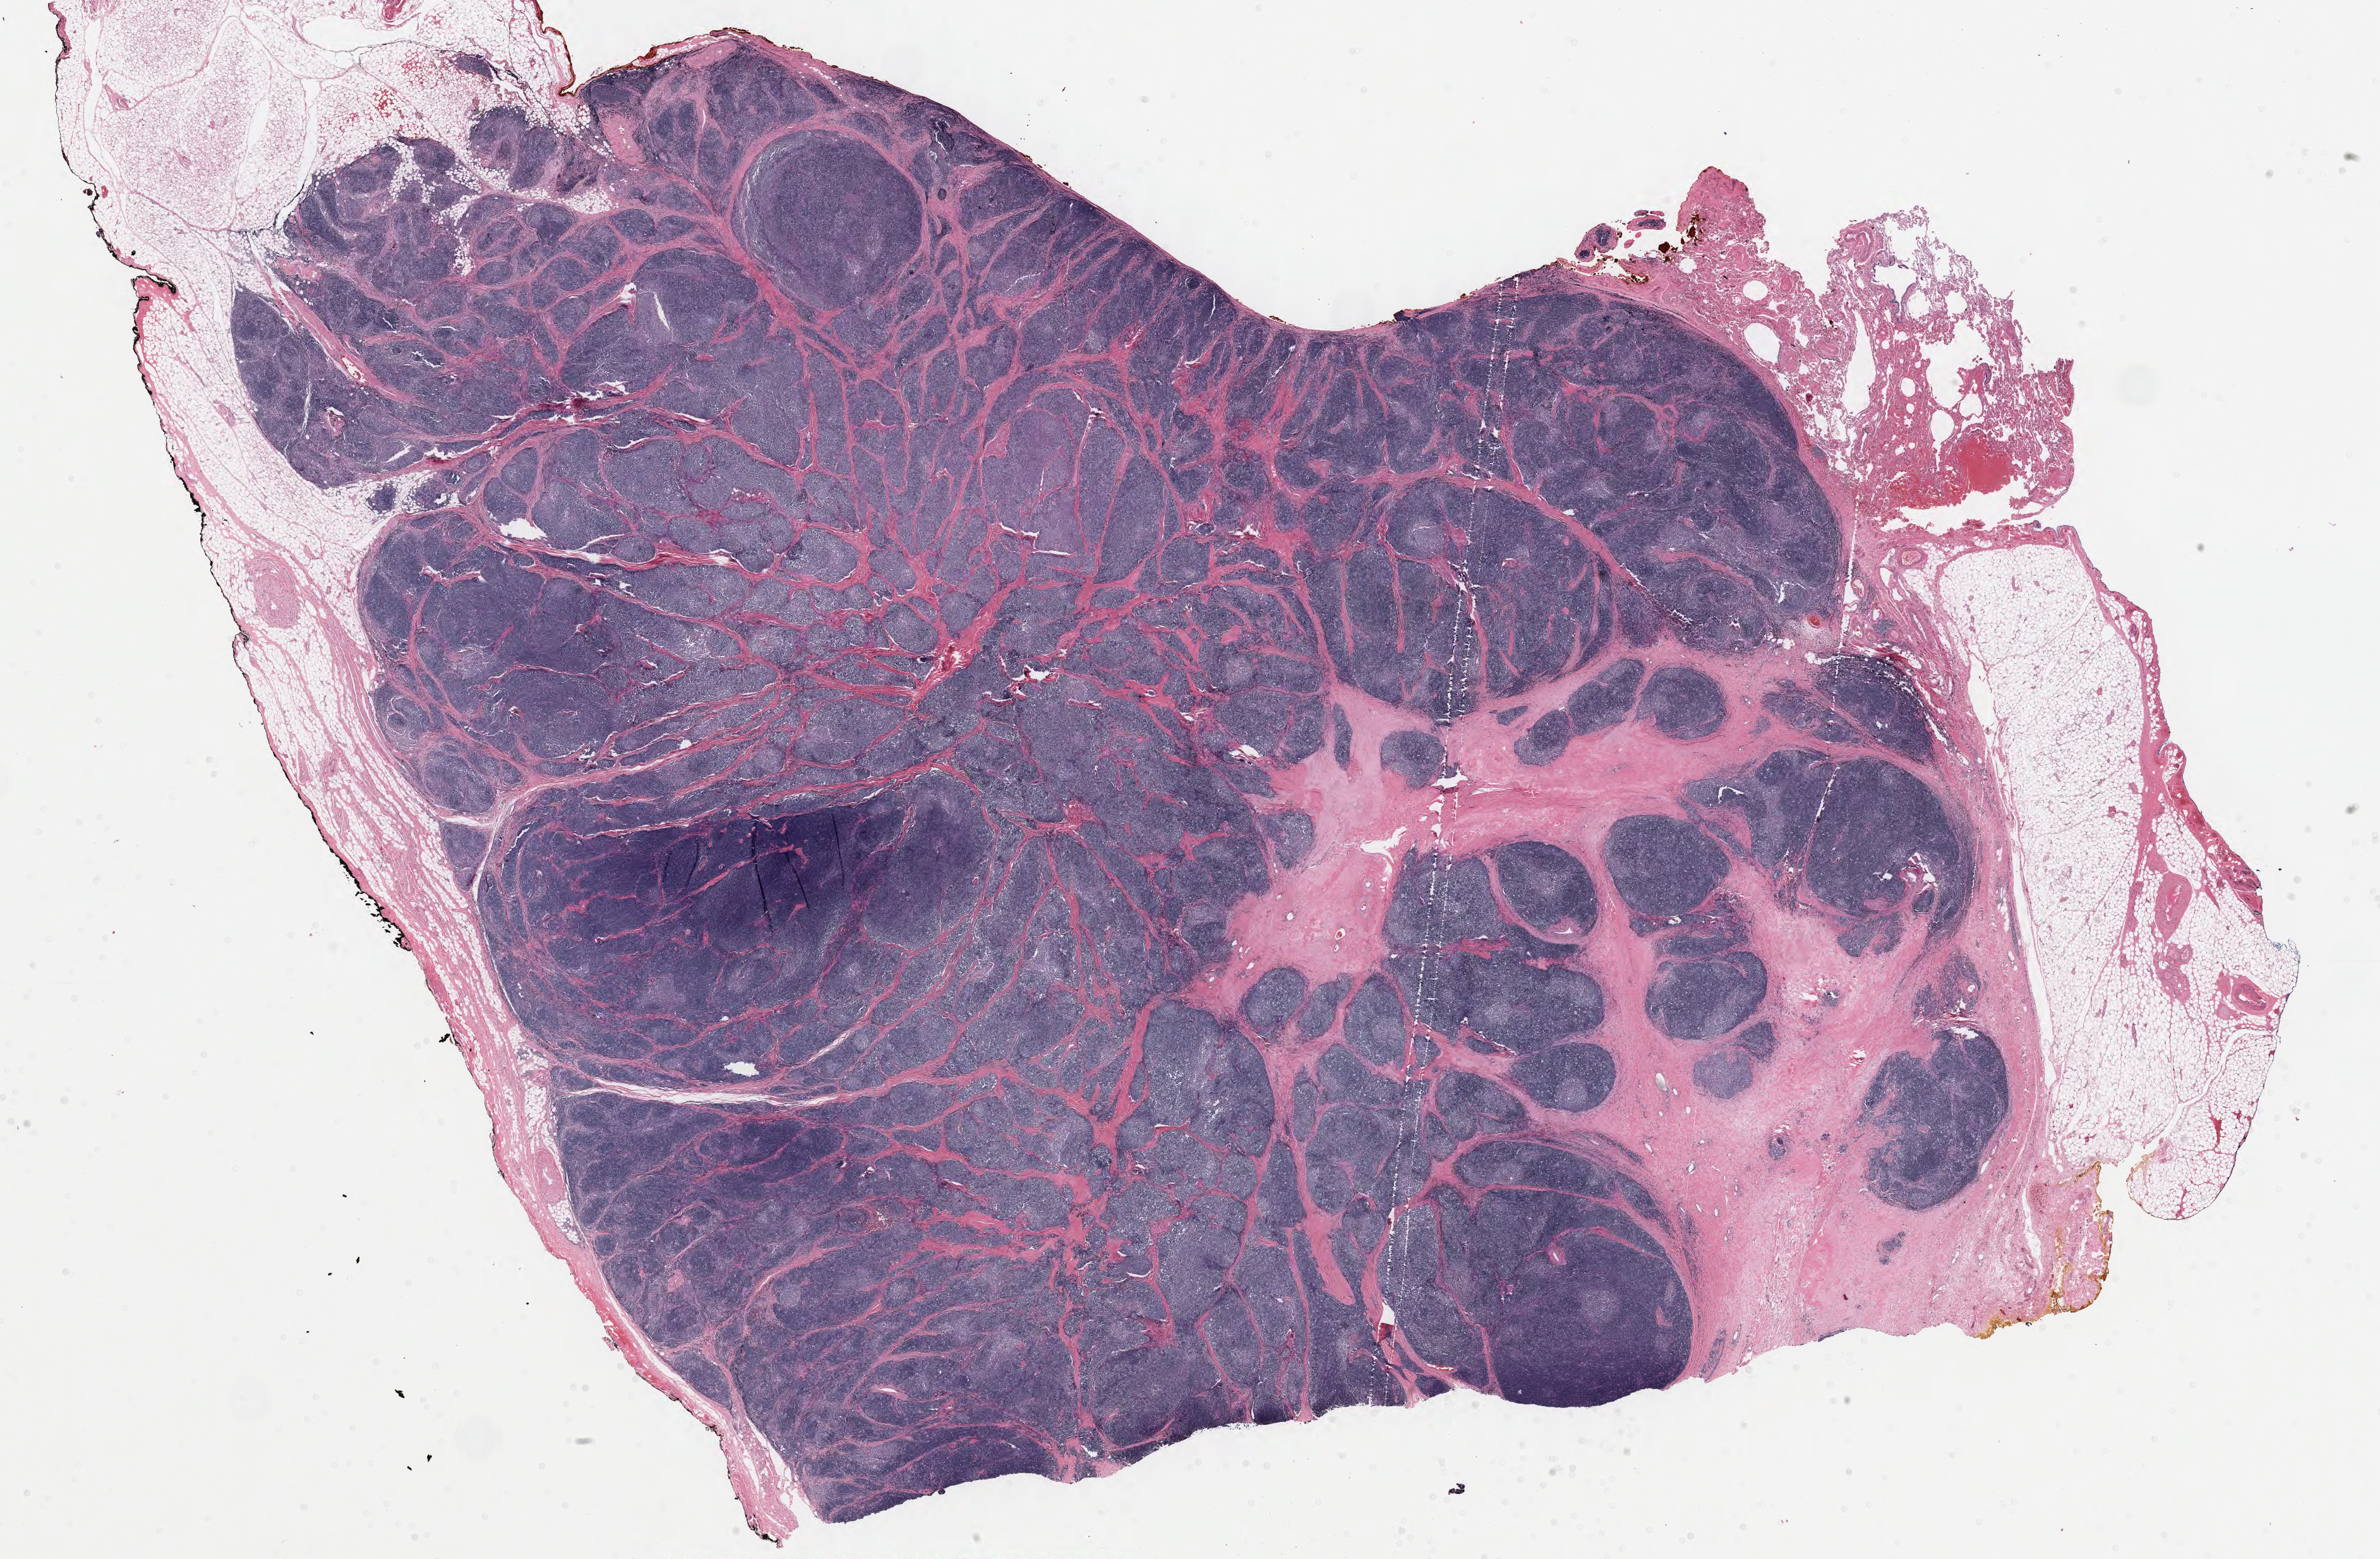
Whole-slide histology image, Hematoxylin and eosin (H&E) stained, whole scanned area (about 29.9 x 19.6 mm, from a 40x scan) shown as a low-resolution overview, formalin-fixed paraffin-embedded (FFPE) diagnostic section, primary tumour sample from the thymus. Female patient; age at initial diagnosis 57 years.
* pathologic diagnosis: Thymoma, type B1, NOS